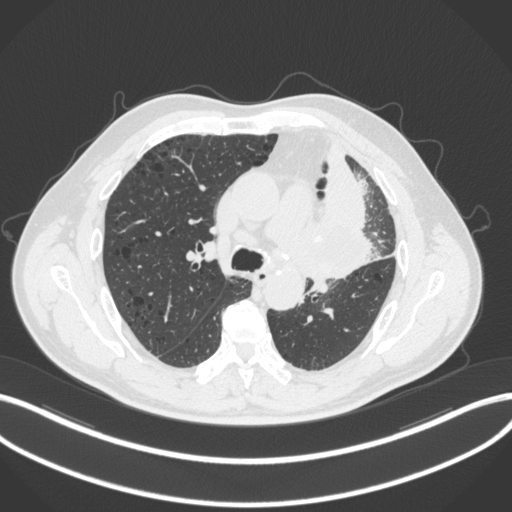
Chest CT, one axial slice; slice 186 of 286 in the series (ordered by position); 120 kVp; lung window (W 1500 / L -600 HU); 1 mm slice thickness; 512 × 512 image matrix. Patient: male, 68 years. Case-level facts recorded for this patient, not image findings: clinical TNM (as recorded): T3 N3 M1.
Outlined on this slice (bounding box drawn by a radiologist):
- lung tumour (recorded histology: adenocarcinoma): bounding box [x1, y1, x2, y2] px = [314, 176, 389, 288]